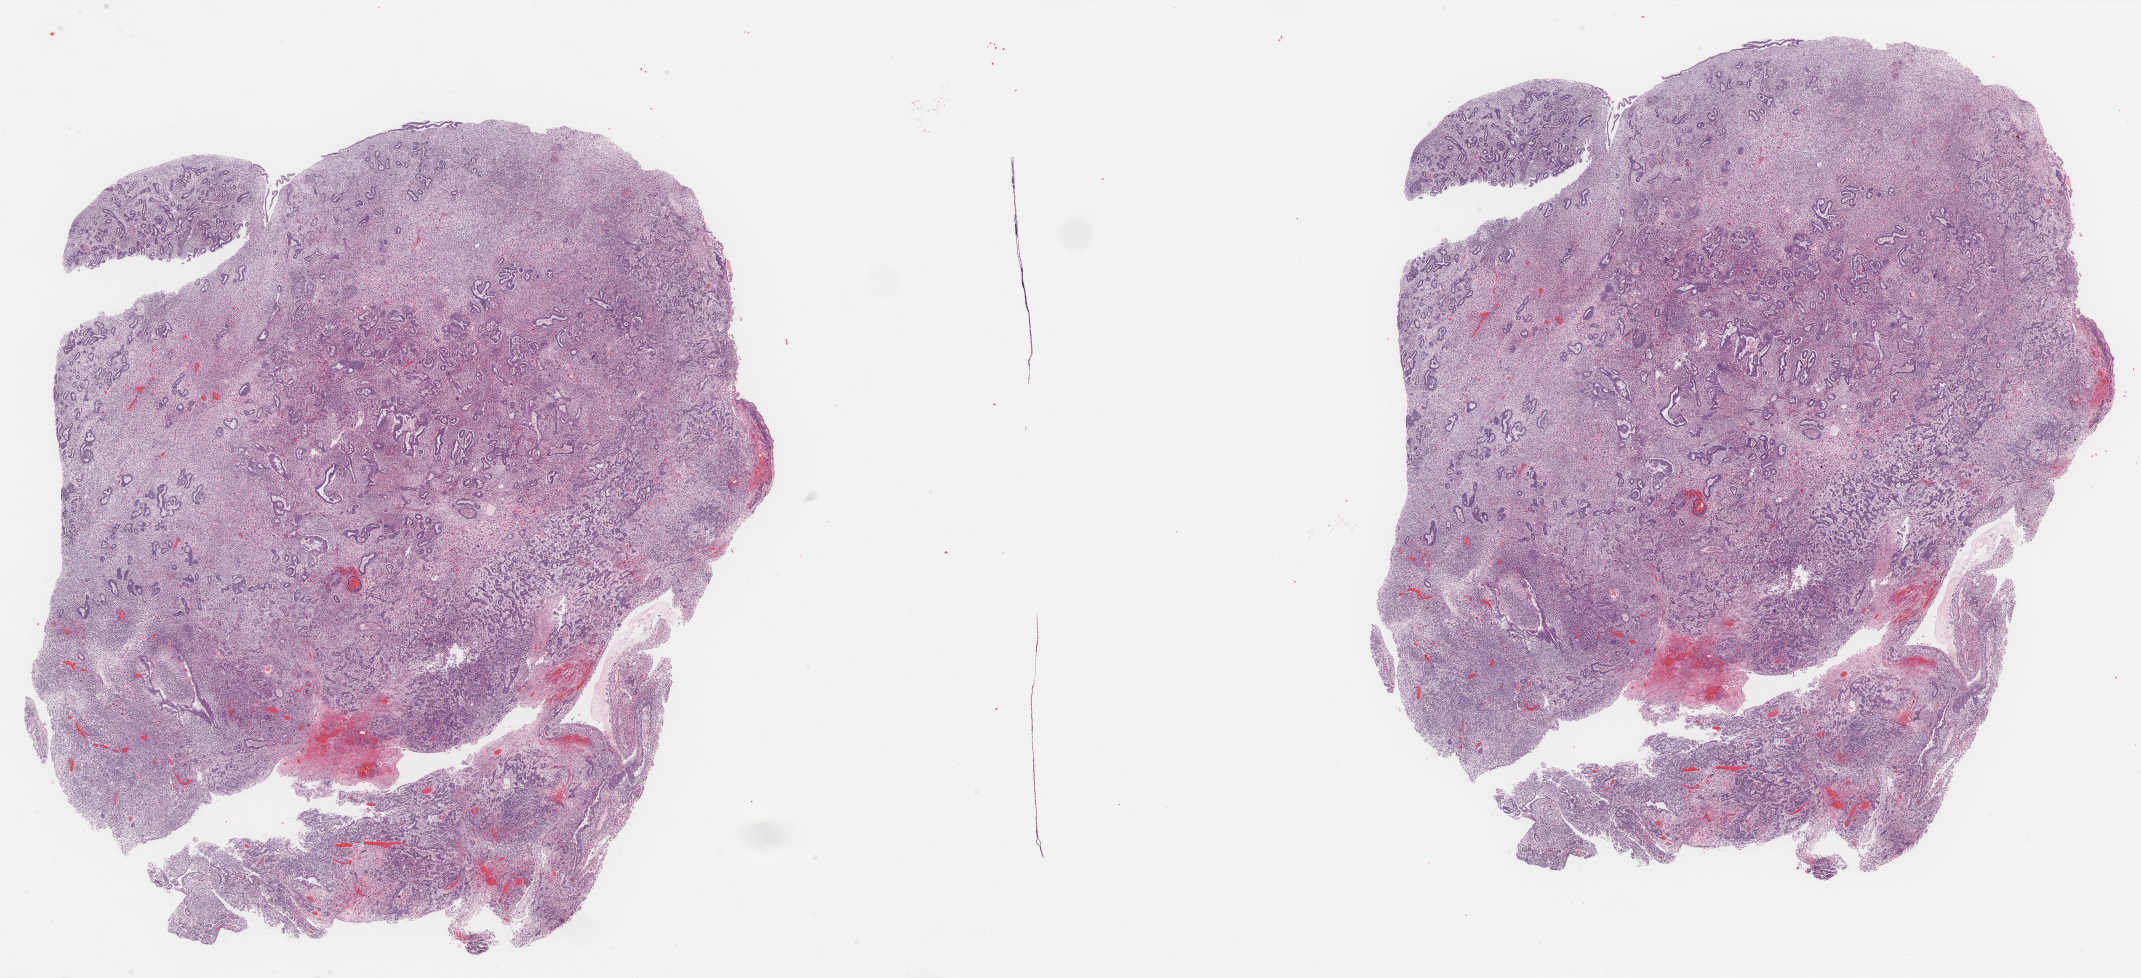
Whole-slide histology image, H&E-stained, low-resolution overview of the scanned area, about 33.9 x 15.5 mm, formalin-fixed paraffin-embedded (FFPE) diagnostic section, primary tumour sample from the uterus. Female patient; age at initial diagnosis 82 years.
Lymph nodes positive (case pathology): 0 of 7 examined. FIGO stage: IA. Histologic diagnosis: Mullerian mixed tumor.